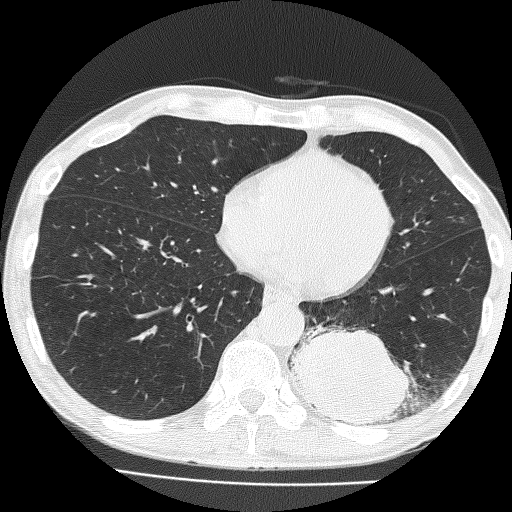
Axial slice from a low-dose chest CT screening exam. First (baseline) screen. Lung window (W 1500 / L -600 HU). Slice 100 of 160 in the series. 512 × 512 image matrix. Male, age 58 years at enrolment. Current smoker at enrolment.
Expert-annotated lung lesion, bounding box [x1, y1, x2, y2] px = [295, 301, 426, 434]. The screening reader recorded 2 non-calcified nodules or masses ≥4 mm on this exam; which of them this box marks is not recorded. Lung cancer was diagnosed 39 days after this screen: non-small cell carcinoma, left lower lobe, poorly differentiated (G3), stage IV (AJCC 6th edition), 74 mm at pathology.